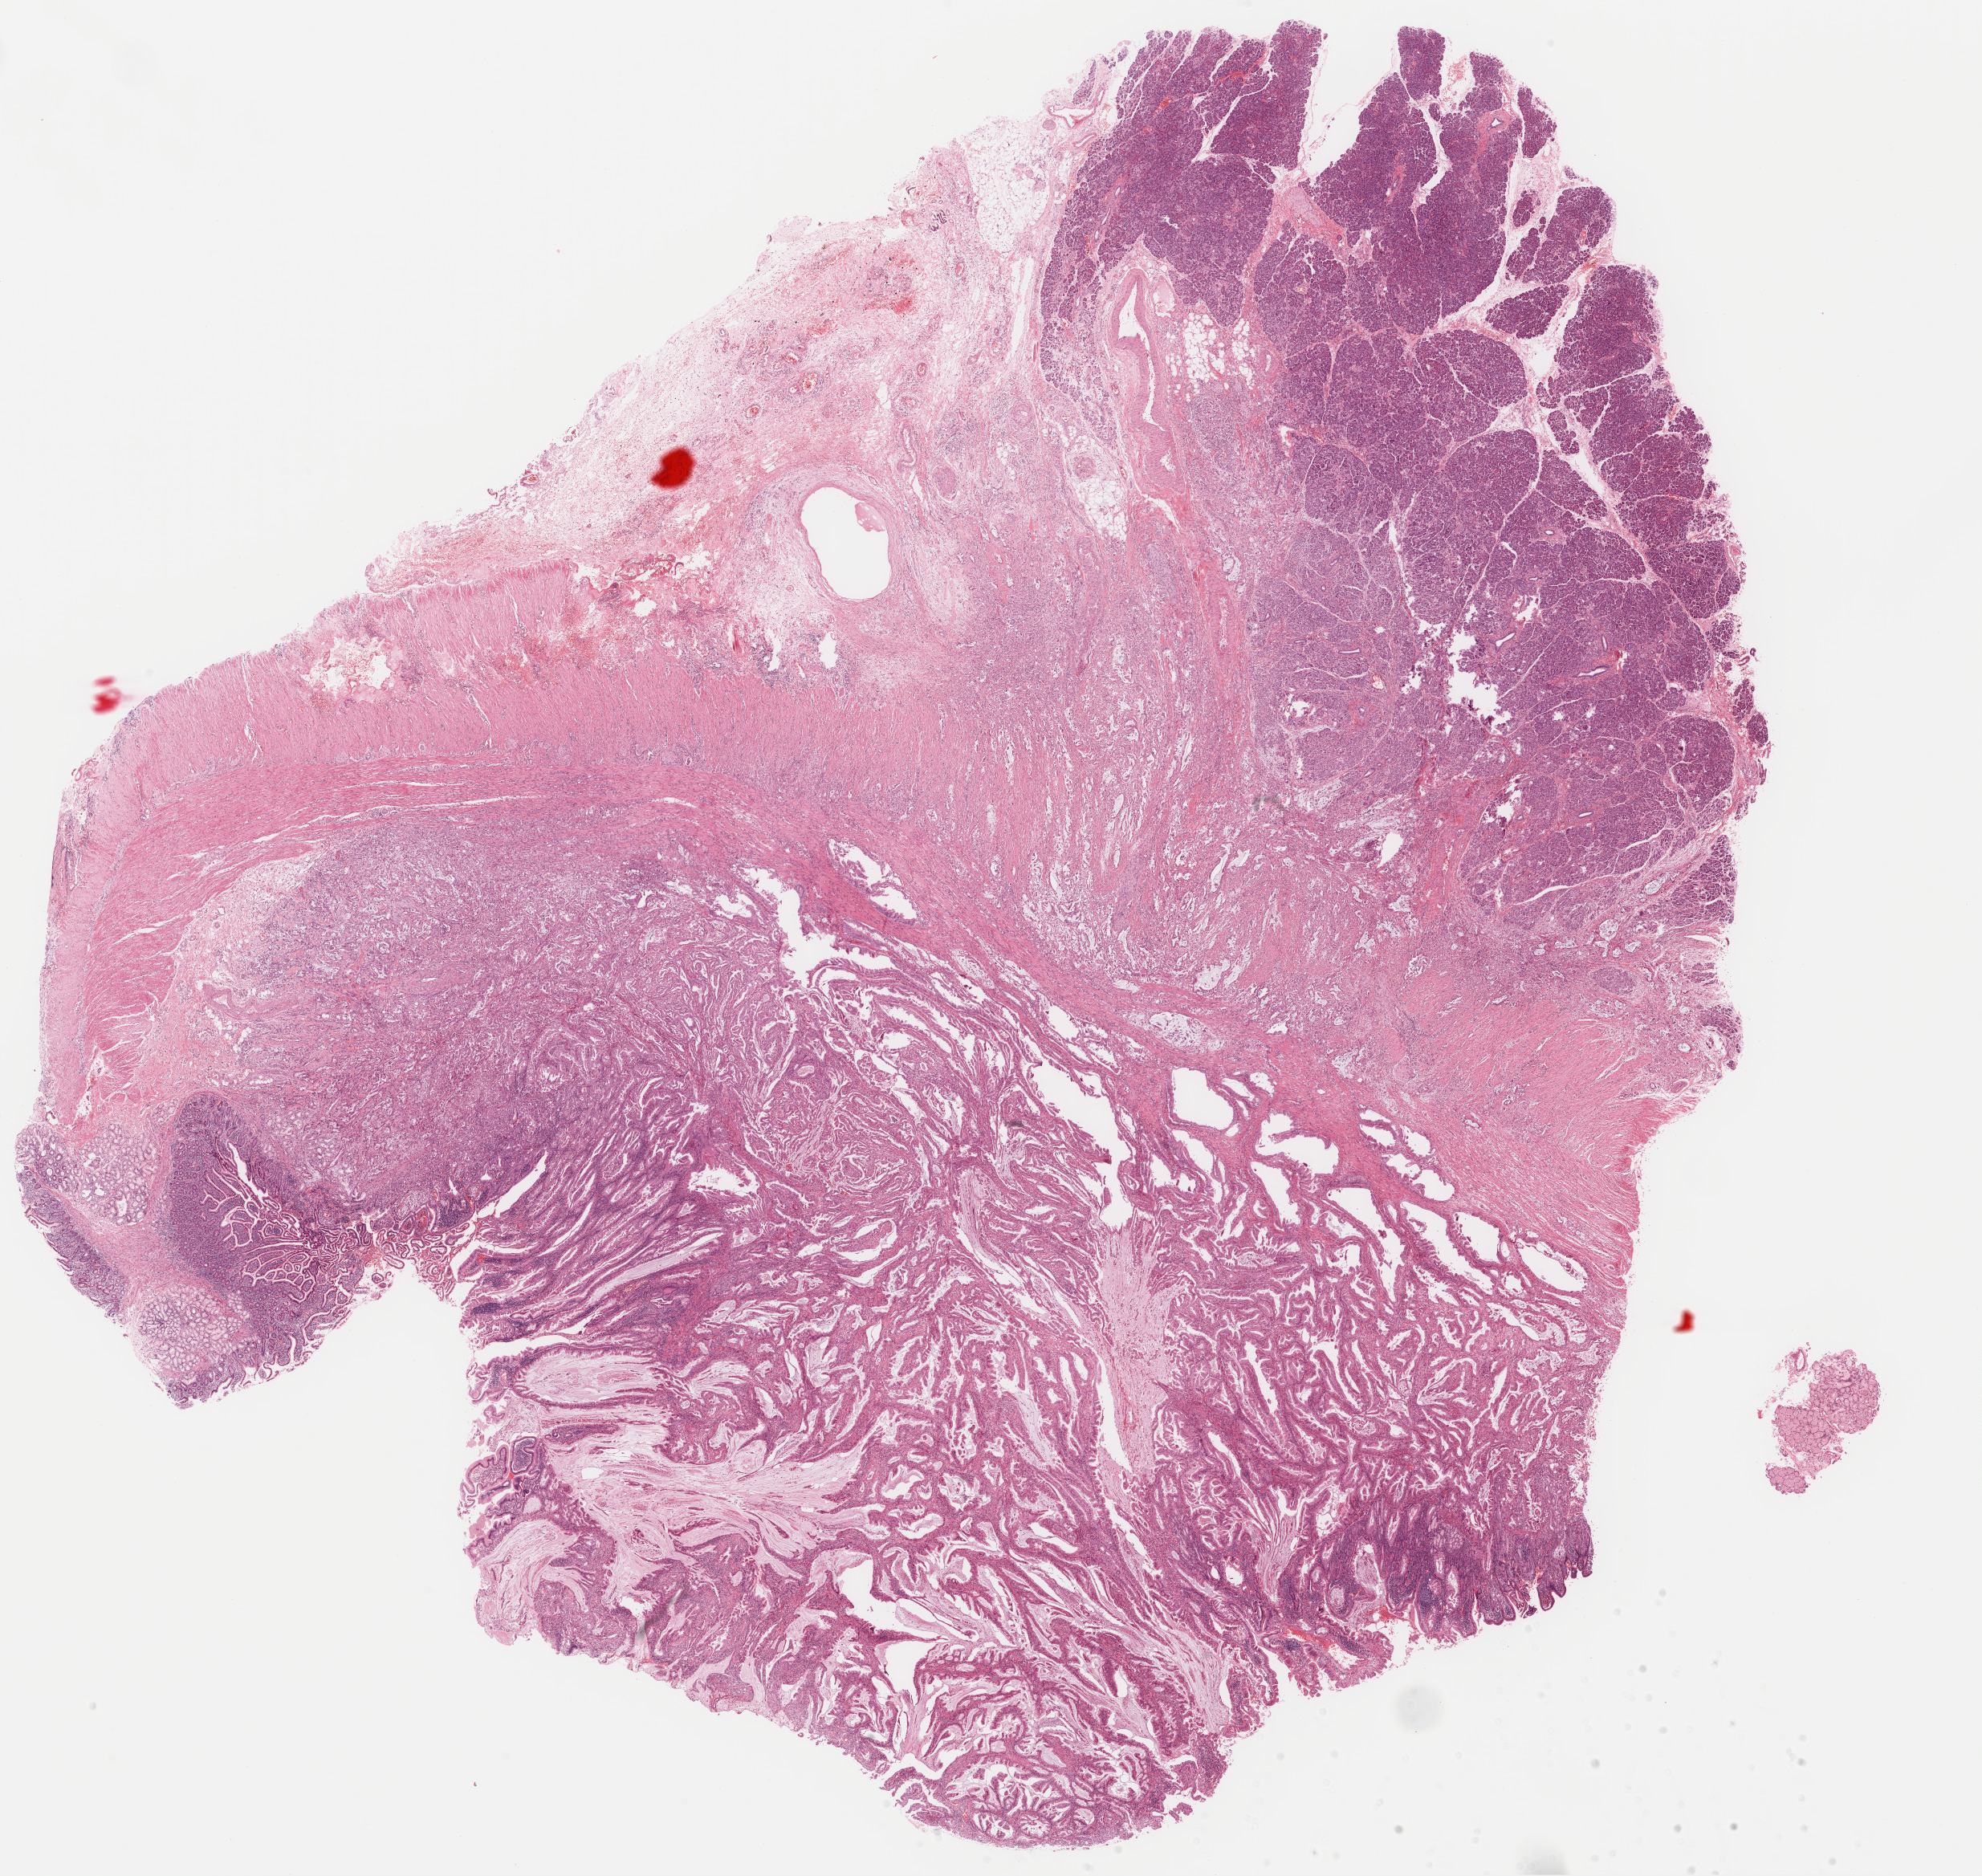
Digitized H&E-stained tissue section (whole slide) — whole scanned area (about 19.5 x 18.5 mm) shown as a low-resolution overview, FFPE section, sample: primary tumour, pancreas. Patient: male, age at initial diagnosis 48 years.
Pathologic diagnosis: Mucinous adenocarcinoma (head of pancreas).